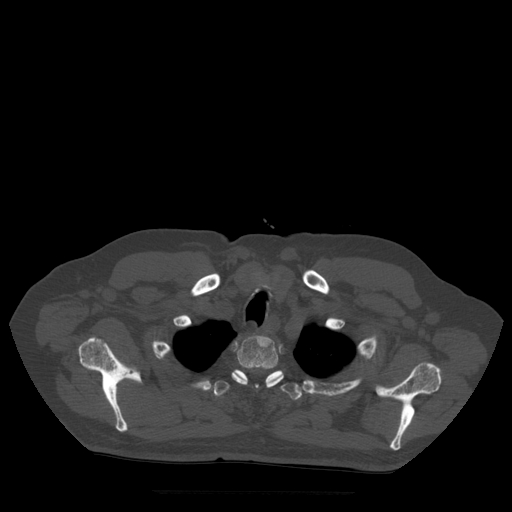
CT including the spine, one axial slice. Position 420 of 522 along the scan axis. Bone window (W 1800 / L 400 HU). 1.25 mm slice thickness. 512 × 512 image matrix, field of view 420 × 420 mm. Patient age 72 years. From the clinical record (not read from this slice): primary cancer: prostate.
Outlined on this slice (semi-automatically segmented with operator editing):
- T2 vertebra: bounding box <232,336,284,388> (left, top, right, bottom; pixels)
- T3 vertebra: <213,370,302,400>